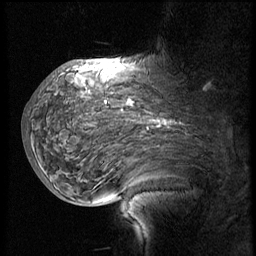
Breast MRI (dynamic contrast-enhanced), one sagittal slice; position 38 of 60 along the scan axis; 3 images stored at this slice position (order not interpretable as contrast timing); 1.5 T; TE 4.2 ms, TR 8.9 ms; 2.5 mm slice thickness; 256 × 256 image matrix, field of view 200 × 200 mm. Patient: female, 57 years. Case-level facts recorded for this patient, not image findings: setting: breast cancer imaged before/during neoadjuvant chemotherapy; receptor status: HER2-positive.
Annotated regions visible in this slice (semi-automatically segmented with operator editing):
- analysis volume of interest (the breast-tissue region the enhancement analysis was run in; not a lesion): box from (x=34, y=75) to (x=214, y=171) px
- tumour enhancement mask (voxels above the 140 % enhancement threshold inside the analysis volume of interest): (x=89, y=91)–(x=168, y=125)